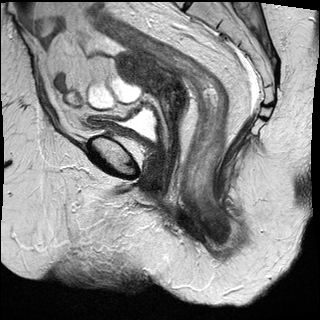
Pelvic MRI for cervical cancer, one sagittal slice; position 14 of 27 along the scan axis; T2-weighted; 1.5 T; TE 89 ms, TR 2740 ms; 4 mm slice thickness; 320 × 320 image matrix, field of view 260 × 260 mm. Female patient, age 67 years.
Annotated regions visible in this slice (expert manual segmentation):
- uterus and cervix: box from (x=116, y=50) to (x=188, y=121) px